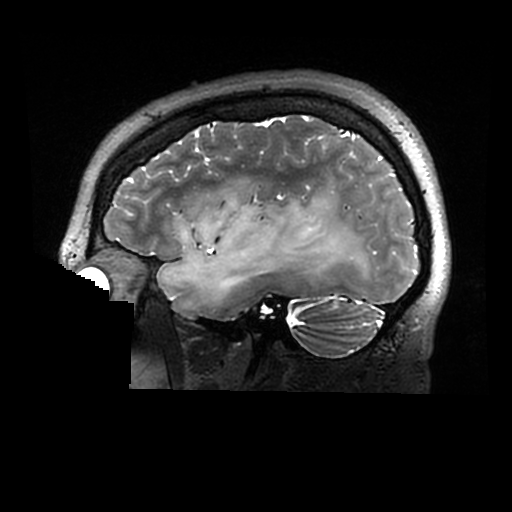
Brain MRI from a brain-tumour surgery series, one sagittal slice; slice 219 of 320 in the series (ordered by position); 0.6 mm slice thickness; 512 × 512 image matrix, field of view 240 × 240 mm. From the clinical record (not read from this slice): histopathology: Astrocytoma; WHO grade: 2; IDH mutation: yes.
Structures marked on this image (expert manual segmentation):
- tumour: bounding box (x1, y1, x2, y2) in pixels: (157, 190, 378, 309)